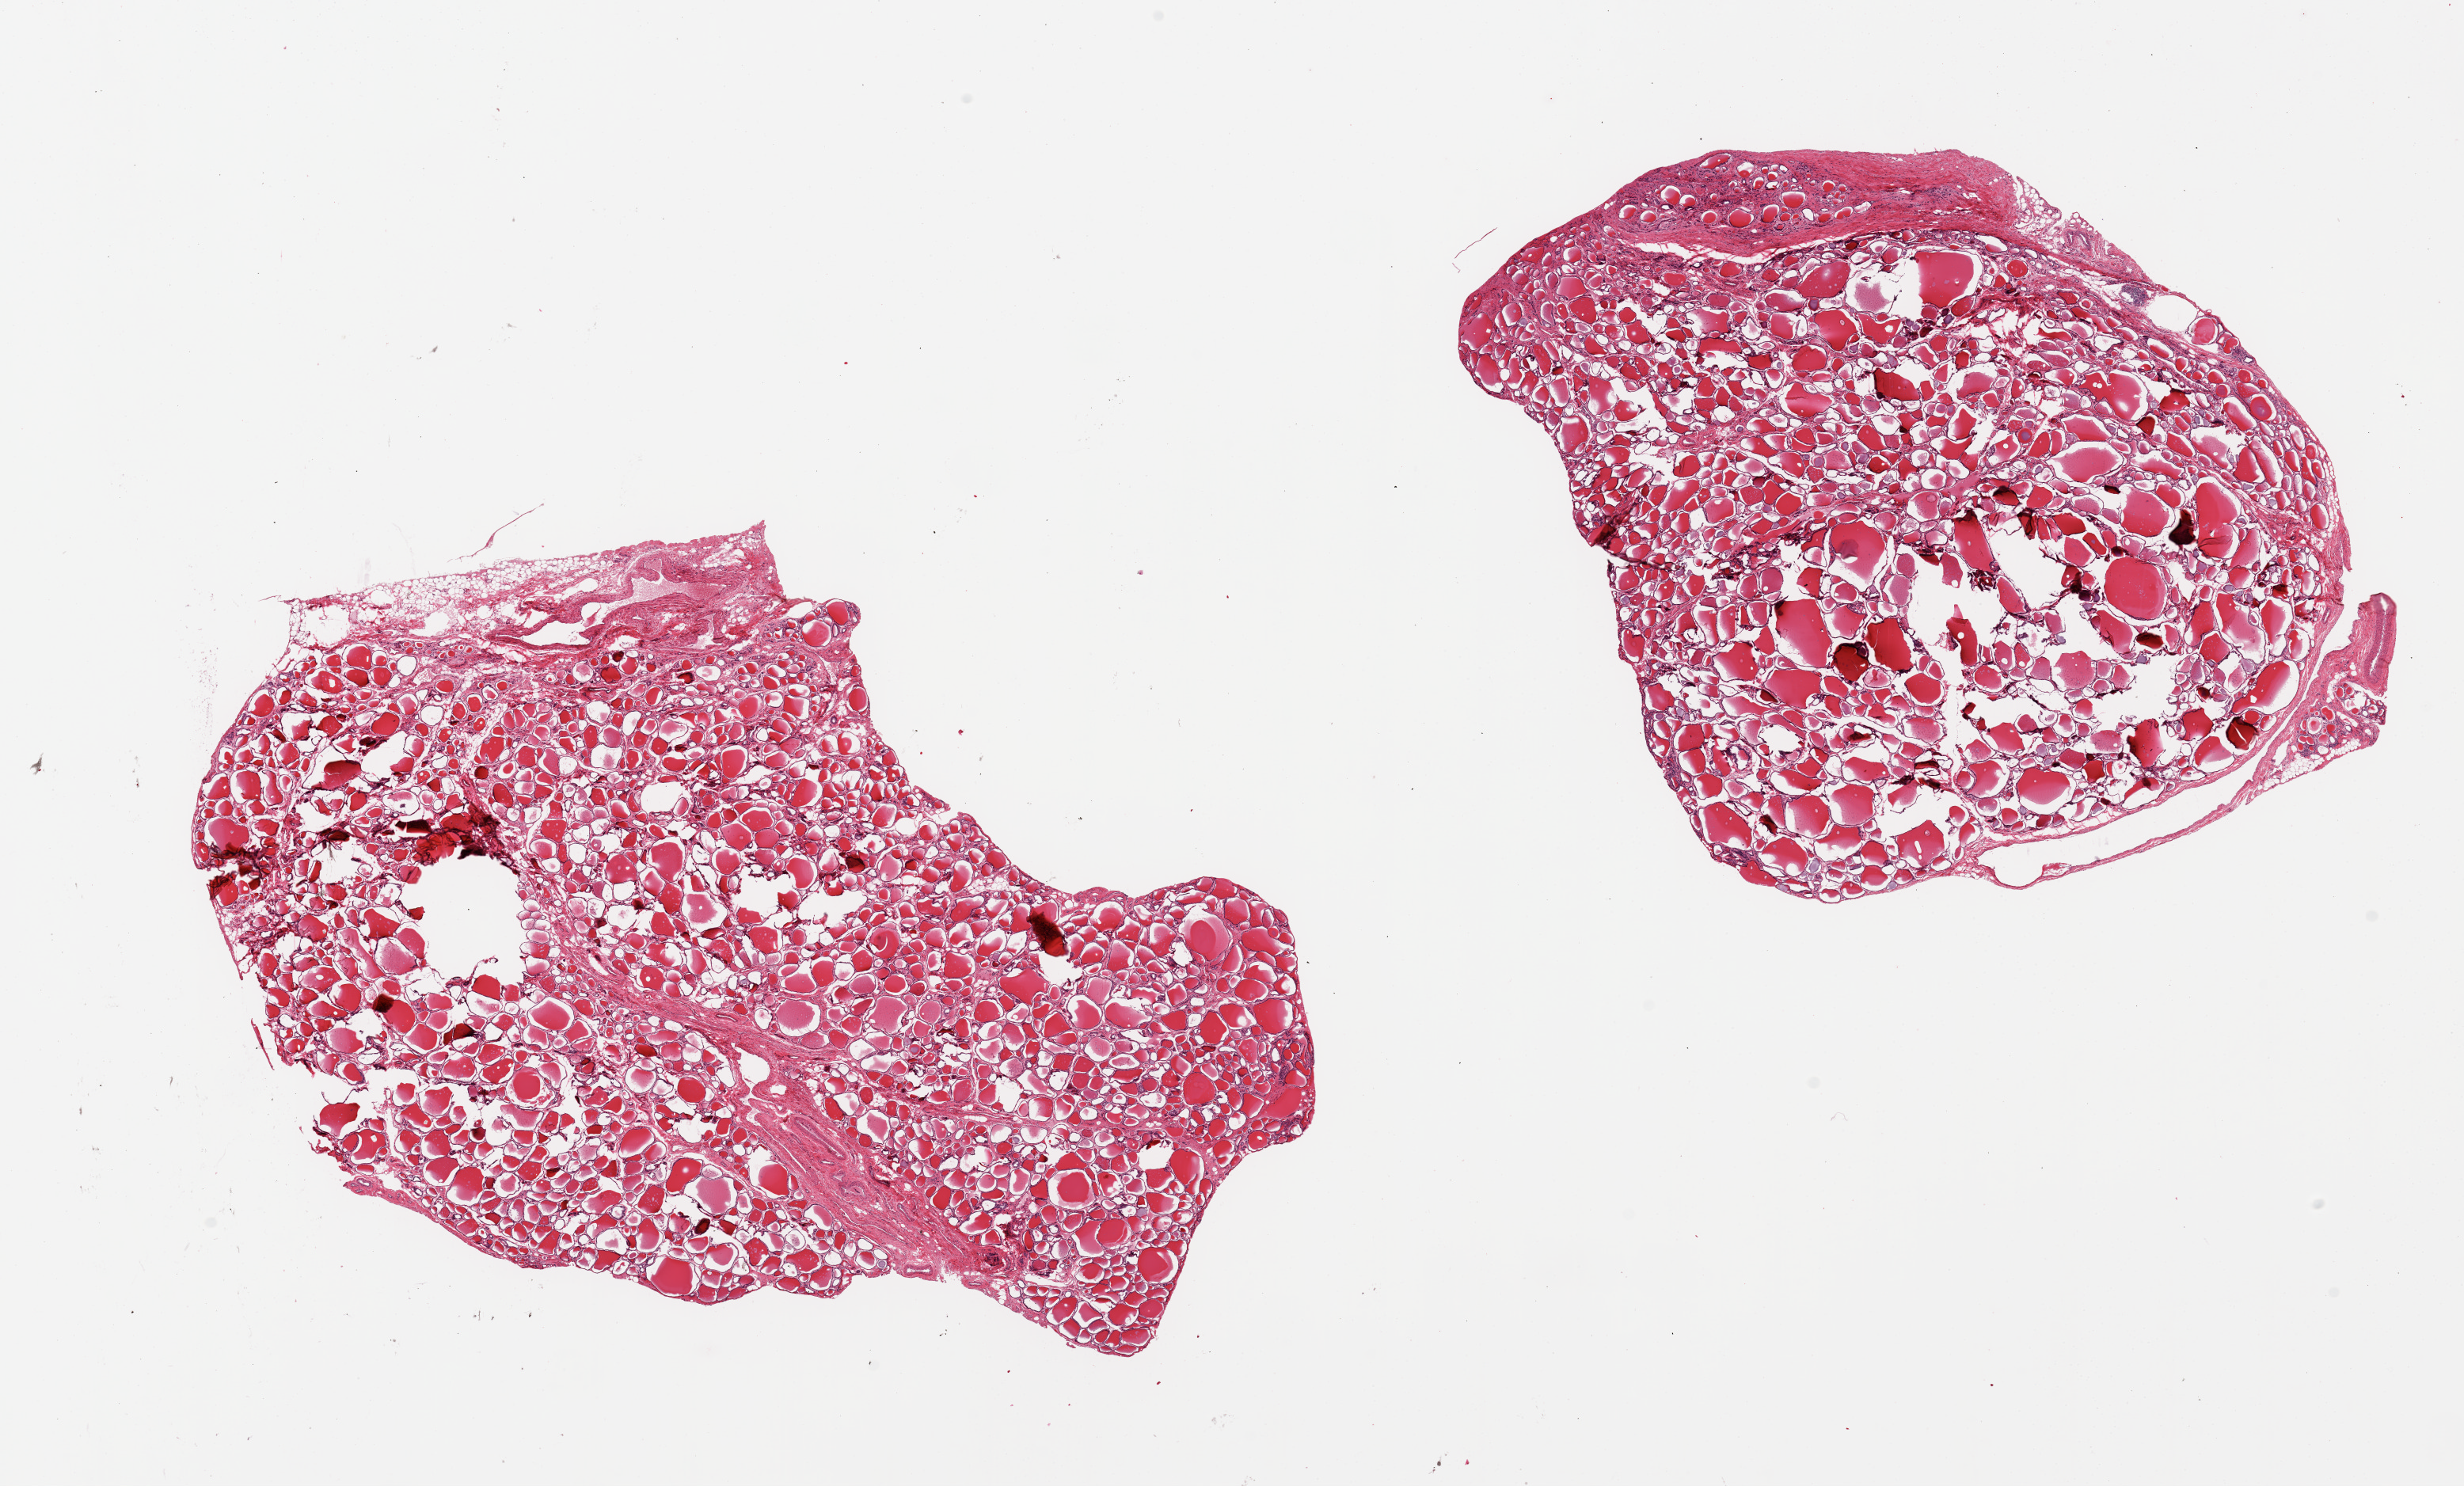
Whole-slide image, hematoxylin and eosin (H&E) stain — a low-resolution overview of the entire scanned area, about 24.6 x 14.8 mm (from a 20x scan); PAXgene-fixed, paraffin-embedded tissue; section of thyroid (target tissue); donor tissue sample.
* pathologist's review note for this sample: 2 pieces, no abnormalities